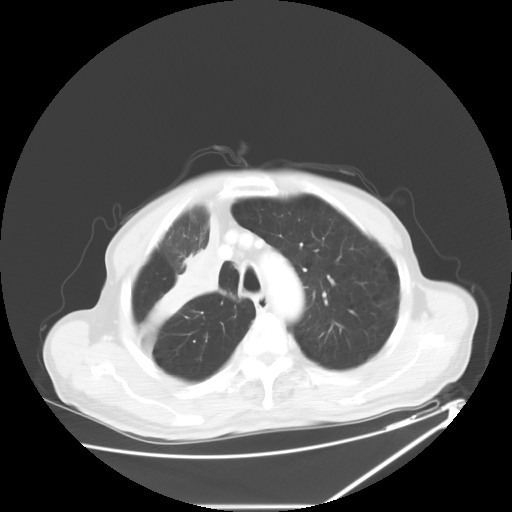
Chest CT, one axial slice; position 48 of 60 along the scan axis; 120 kVp; lung window (W 1500 / L -600 HU); 5 mm slice thickness; 512 × 512 image matrix, field of view 410 × 410 mm. Patient: male, 73 years. Case-level facts recorded for this patient, not image findings: clinical TNM (as recorded): T2a N1 M0.
Structures marked on this image (bounding box drawn by a radiologist):
- lung tumour (recorded histology: squamous cell carcinoma): bounding box [x1, y1, x2, y2] px = [154, 213, 224, 325]